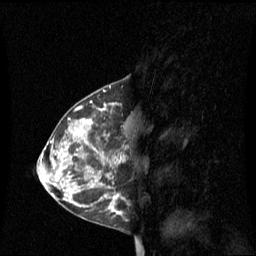
Breast MRI (dynamic contrast-enhanced), one sagittal slice. Position 34 of 60 along the scan axis. Dynamic contrast-enhanced series, image 2 of 3 at this slice position (ordered by acquisition). 1.5 T. TE 4.2 ms, TR 8.4 ms. 2.1 mm slice thickness. 256 × 256 image matrix, field of view 240 × 240 mm. Patient: female, 42 years. From the clinical record (not read from this slice): setting: breast cancer imaged before/during neoadjuvant chemotherapy; receptor status: HR-positive, HER2-negative.
Annotated regions visible in this slice (semi-automatically segmented with operator editing):
- analysis volume of interest (the breast-tissue region the enhancement analysis was run in; not a lesion): bounding box (x1, y1, x2, y2) in pixels: (68, 104, 127, 201)
- tumour enhancement mask (voxels above the 70 % enhancement threshold inside the analysis volume of interest): (112, 194, 119, 201)